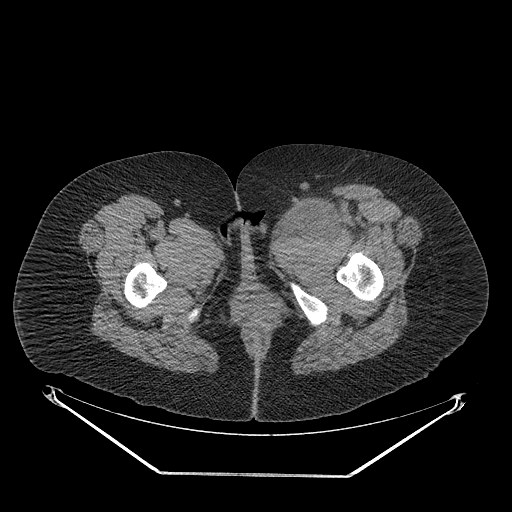
CT of an extremity soft-tissue mass (from a PET/CT study), one axial slice. Reconstruction kernel STANDARD. Soft-tissue window (W 400 / L 40 HU). 3.75 mm slice thickness. 512 × 512 image matrix. Female patient. From the clinical record (not read from this slice): histological type: myxofibrosarcoma; grade: intermediate; site of the primary tumour: left thigh.
Annotated regions visible in this slice (expert contour drawn on MRI and transferred to this co-registered scan by the dataset authors):
- gross tumour volume including surrounding oedema: box from (x=265, y=201) to (x=360, y=254) px
- gross tumour volume (mass): (x=281, y=201)–(x=339, y=239)